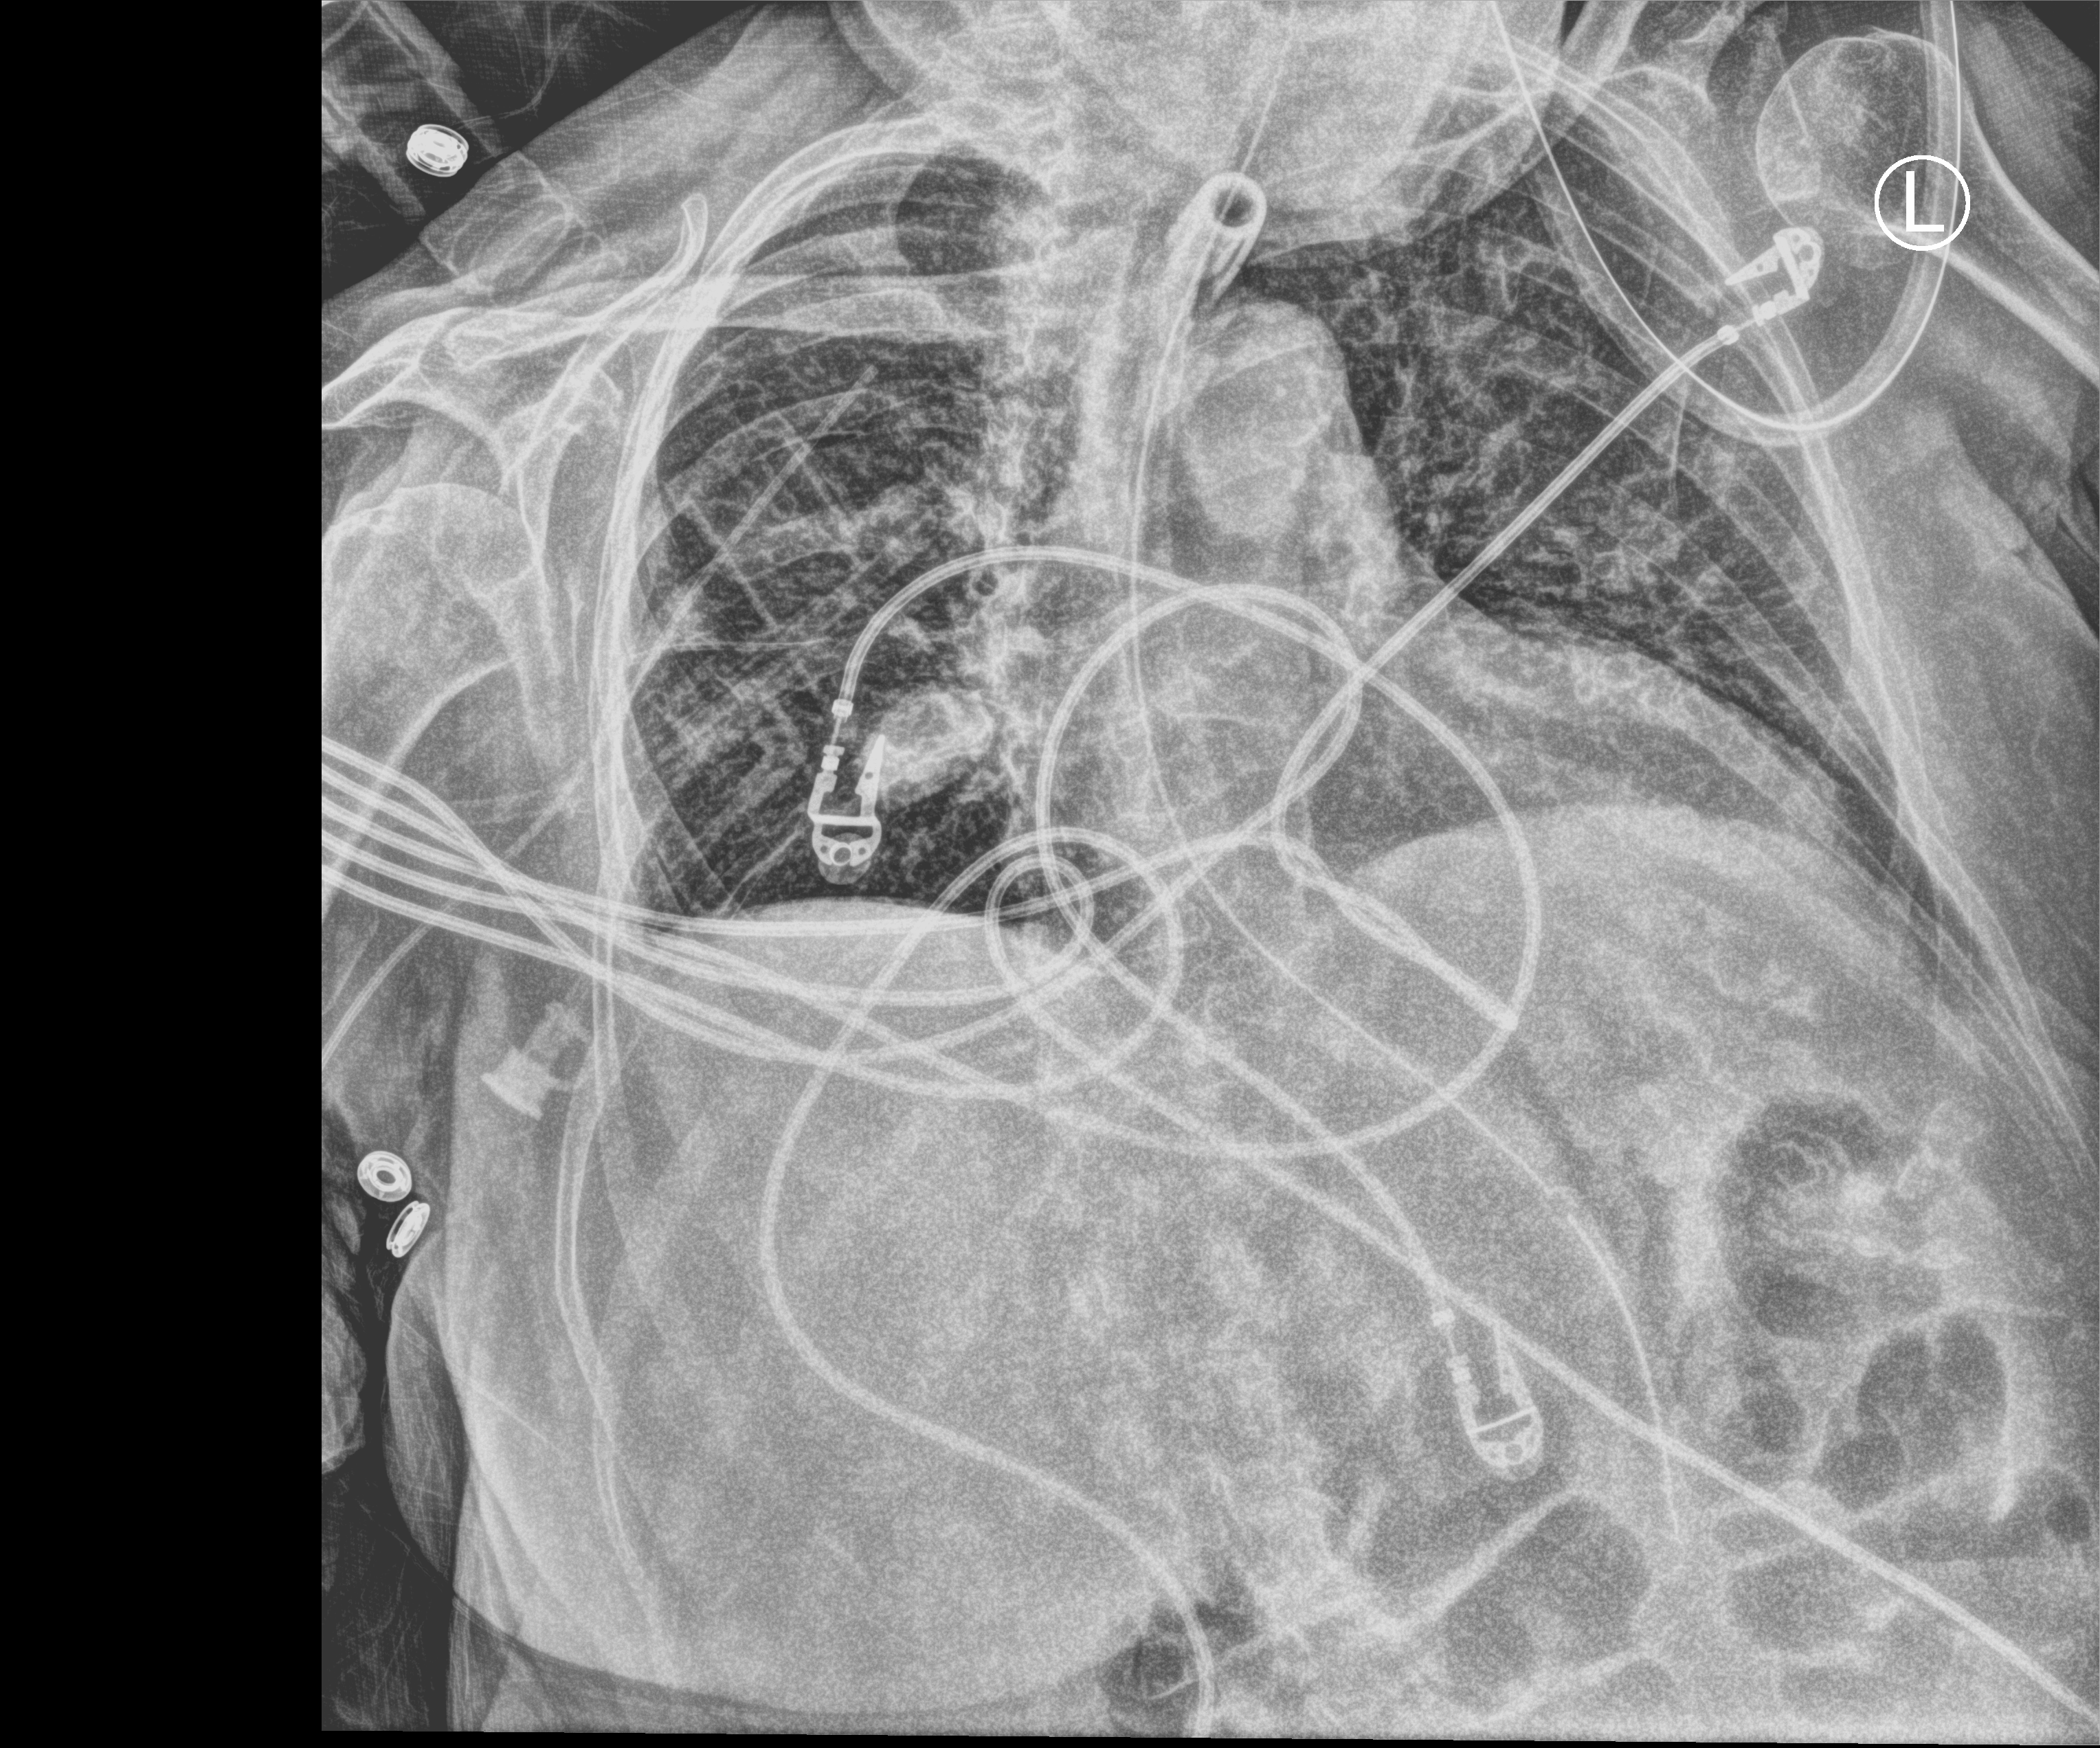
Chest X-ray (portable); anteroposterior (AP) projection. Female patient hospitalised with COVID-19, age 75–90 years.
Hospital-stay facts (about this admission, not read from this image; timing relative to this image not recorded):
- length of hospital stay: 82 days